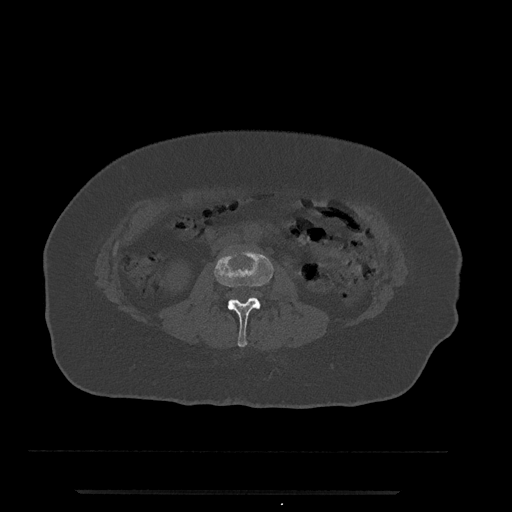
CT including the spine, one axial slice. Position 17 of 797 along the scan axis. Reconstruction kernel Br40s/3. Bone window (W 1800 / L 400 HU). 0.5 mm slice thickness. 512 × 512 image matrix, field of view 440 × 440 mm. Female patient, age 51 years. From the clinical record (not read from this slice): primary cancer: neuro; vertebrae with lytic lesions (as recorded): T8.
Structures marked on this image (semi-automatic segmentation, software-assisted and operator-edited):
- L2 vertebra: bounding box (x1, y1, x2, y2) in pixels: (214, 249, 274, 347)